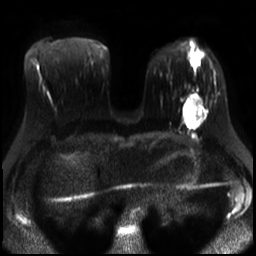
Breast MRI, one axial slice. Slice 11 of 30 in the series (ordered by position). Diffusion-weighted series; image 2 of 4 stored at this slice position (different b-values; order by instance number). 3 T. 4 mm slice thickness. 256 × 256 image matrix, field of view 320 × 320 mm. Female patient.
Annotated regions visible in this slice (expert manual segmentation):
- tumour on diffusion-weighted imaging: bounding box (x1, y1, x2, y2) in pixels: (183, 95, 197, 126)